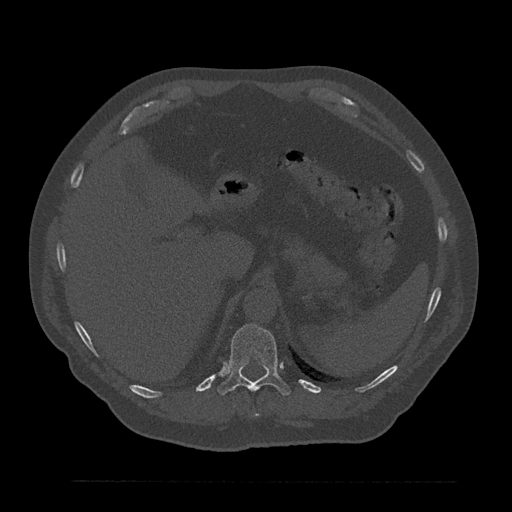
CT including the spine, one axial slice. Position 299 of 797 along the scan axis. Reconstruction kernel Br40s/3. Bone window (W 1800 / L 400 HU). 0.5 mm slice thickness. 512 × 512 image matrix. Patient: male, 61 years. From the clinical record (not read from this slice): primary cancer: prostate.
Structures marked on this image (semi-automatic segmentation, software-assisted and operator-edited):
- T10 vertebra: bounding box (x1, y1, x2, y2) in pixels: (255, 414, 260, 417)
- T11 vertebra: (217, 324, 290, 396)